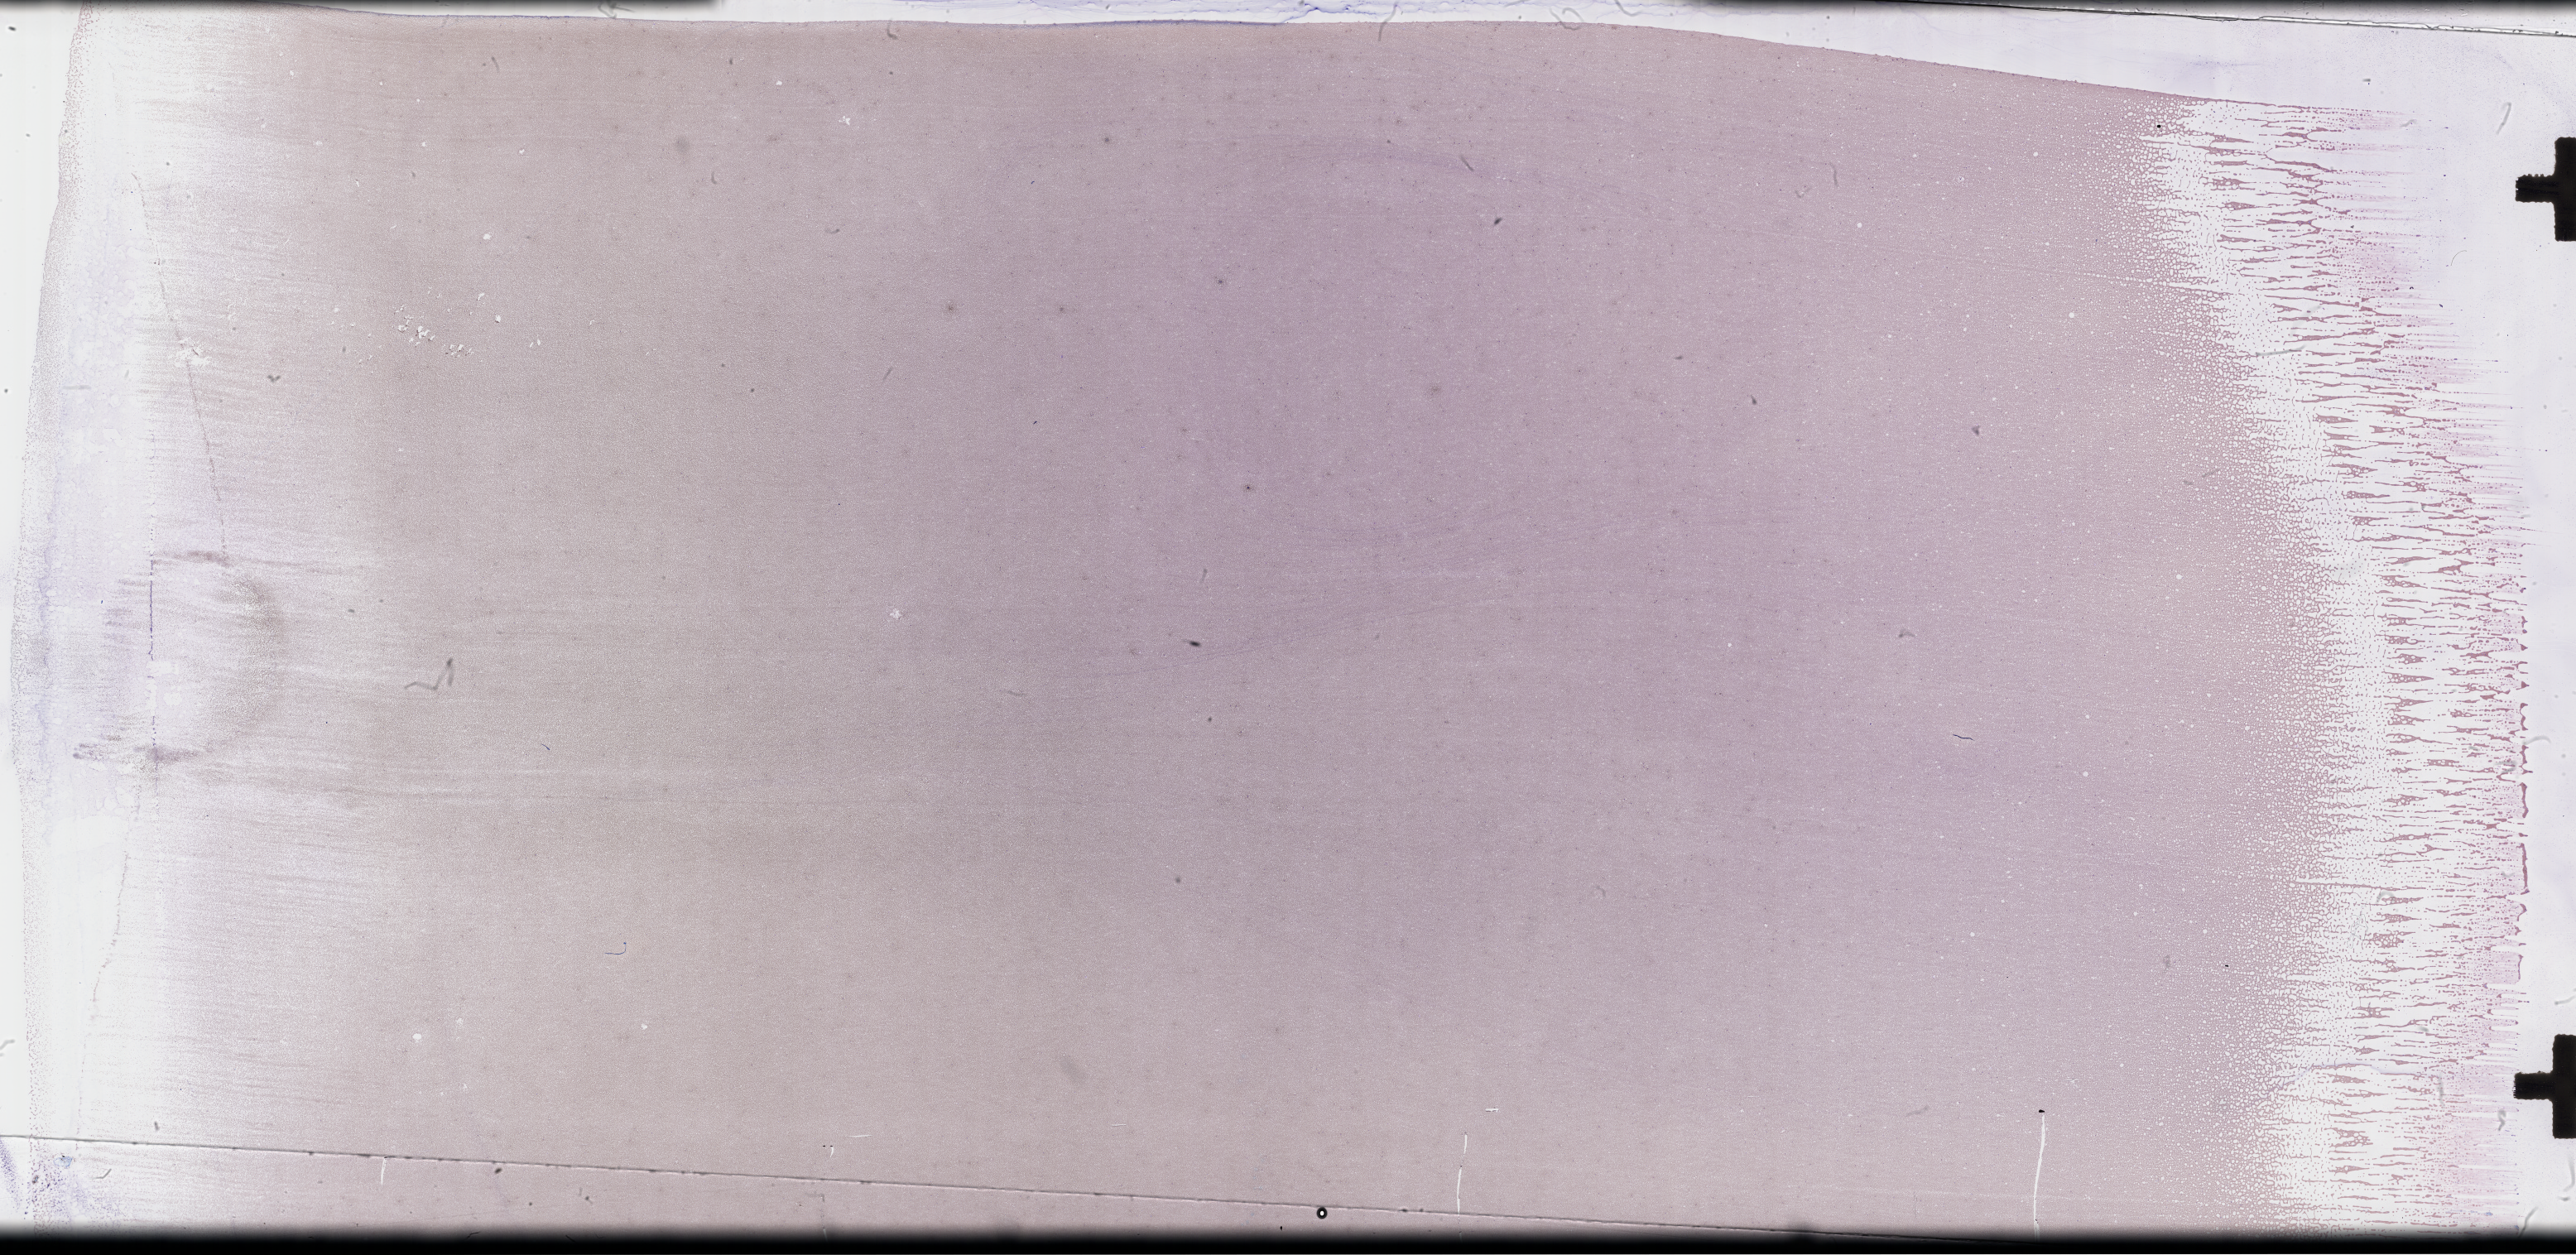
Wright-Giemsa-stained whole blood smear, whole-slide image, whole scanned area (about 50.3 x 24.5 mm) shown as a low-resolution overview. Specimen time point: collected on treatment. Male patient.
• from a patient with: Plasma Cell Myeloma